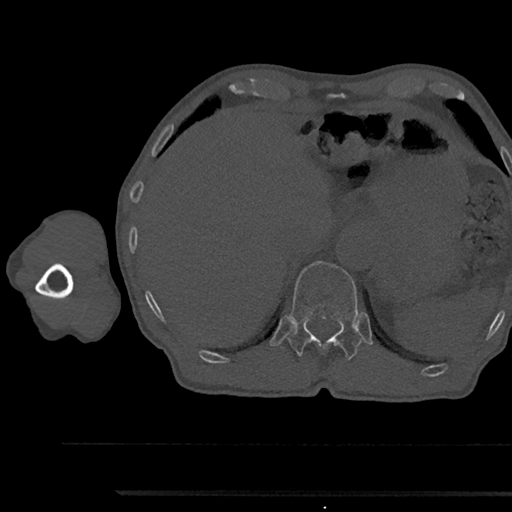
CT including the spine, one axial slice. Slice 724 of 797 in the series (ordered by position). Reconstruction kernel Br40s/3. Bone window (W 1800 / L 400 HU). 512 × 512 image matrix, field of view 367 × 367 mm. Male patient, age 79 years. From the clinical record (not read from this slice): primary cancer: prostate.
Annotated regions visible in this slice (semi-automatic segmentation, software-assisted and operator-edited):
- T12 vertebra: bounding box (x1, y1, x2, y2) in pixels: (288, 261, 362, 359)